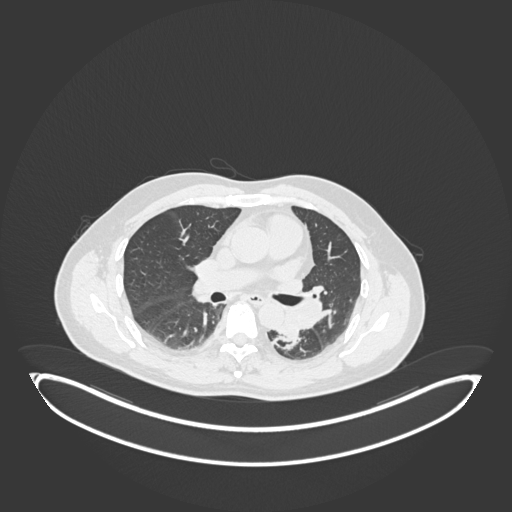
Chest CT, one axial slice; position 113 of 258 along the scan axis; lung window (W 1500 / L -600 HU); 1 mm slice thickness; 512 × 512 image matrix, field of view 500 × 500 mm. Patient: male, 54 years. Case-level facts recorded for this patient, not image findings: clinical TNM (as recorded): T3 N0 M0.
Annotated regions visible in this slice (rectangle marked by the reading radiologist):
- lung tumour (recorded histology: squamous cell carcinoma): box from (x=277, y=305) to (x=305, y=343) px